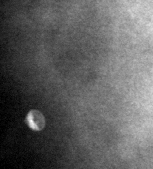
Cropped region of a digitized screen-film mammogram centred on a radiologist-marked abnormality; right breast; MLO view.
Calcifications, morphology lucent center; BI-RADS assessment category 2; subtlety rating 3 on a 1 (subtle) to 5 (obvious) scale; benign; no additional work-up was recommended (benign without callback).